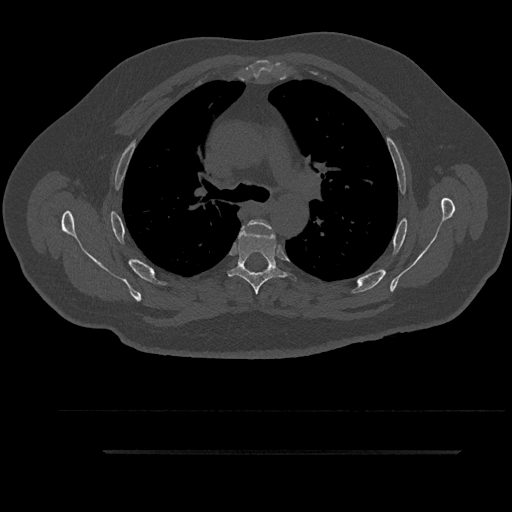
CT including the spine, one axial slice. Slice 632 of 797 in the series (ordered by position). Bone window (W 1800 / L 400 HU). 512 × 512 image matrix, field of view 432 × 432 mm. Patient: male, 63 years. From the clinical record (not read from this slice): primary cancer: renal.
Outlined on this slice (semi-automatic segmentation, software-assisted and operator-edited):
- T4 vertebra: box from (x=243, y=219) to (x=272, y=230) px
- T5 vertebra: (x=227, y=225)–(x=297, y=295)
- T6 vertebra: (x=261, y=270)–(x=266, y=273)